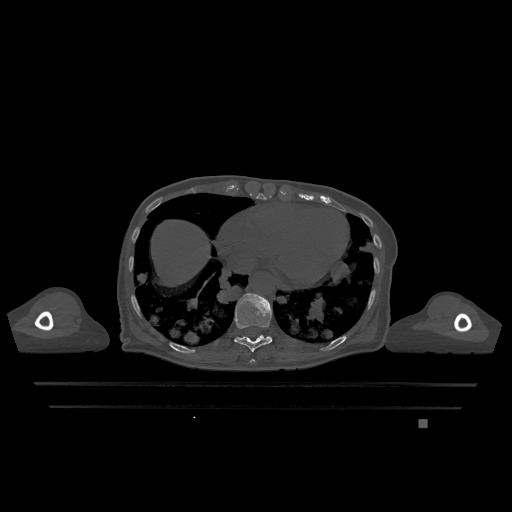
CT including the spine, one axial slice. Bone window (W 1800 / L 400 HU). 0.5 mm slice thickness. 512 × 512 image matrix, field of view 500 × 500 mm. Female patient, age 74 years. From the clinical record (not read from this slice): primary cancer: lung; vertebrae with lytic lesions (as recorded): T1, T4, T5, T6, L4, L5.
Annotated regions visible in this slice (semi-automatic segmentation, software-assisted and operator-edited):
- T10 vertebra: bounding box [x1, y1, x2, y2] px = [234, 293, 272, 352]
- T9 vertebra: [250, 359, 256, 363]